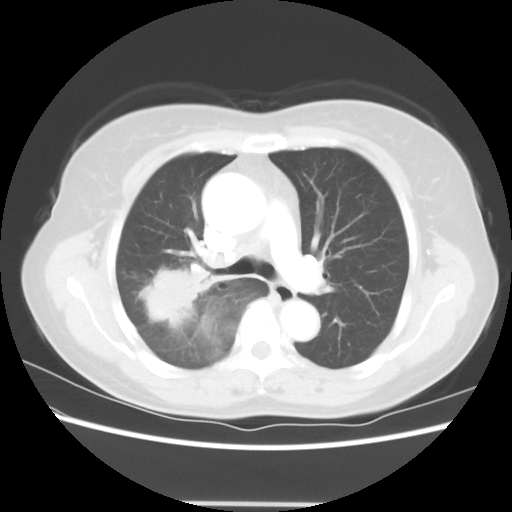
Chest CT, one axial slice. Position 38 of 56 along the scan axis. Lung window (W 1500 / L -600 HU). 5 mm slice thickness. 512 × 512 image matrix. Patient: female, 55 years. Case-level facts recorded for this patient, not image findings: clinical TNM (as recorded): T2 N1 M0.
Annotated regions visible in this slice (bounding box drawn by a radiologist):
- lung tumour (recorded histology: adenocarcinoma): box from (x=127, y=253) to (x=216, y=327) px